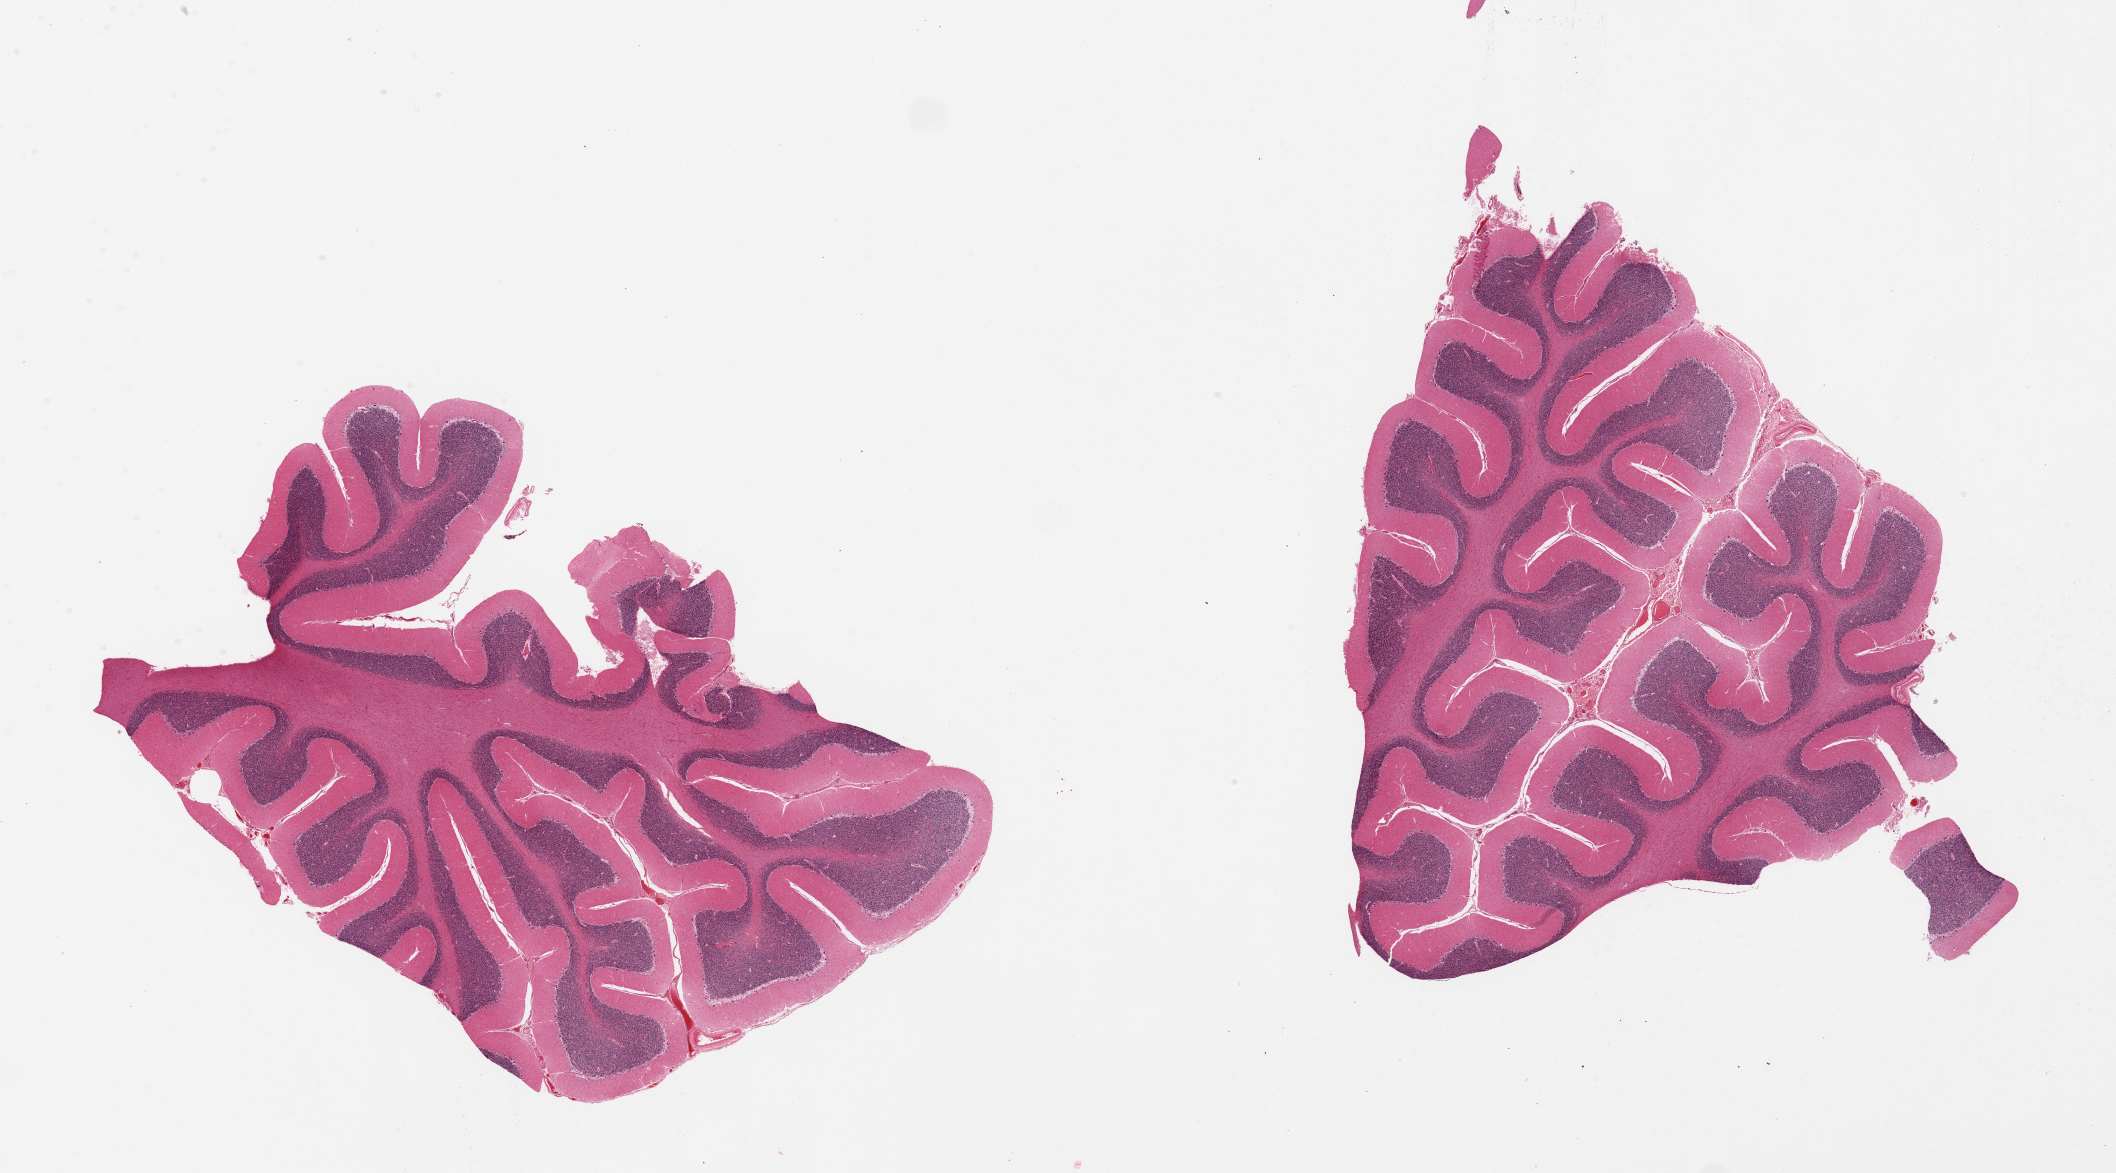
Hematoxylin and eosin (H&E) whole-slide image — shown as a low-resolution overview of the whole scanned area (about 33.5 x 18.6 mm, acquisition: 20x scan), PAXgene-fixed paraffin-embedded (PFPE) section, section of cerebellum (target tissue), donor tissue sample. Male donor.
Review note (as recorded): 2 pieces, no abnormalities.